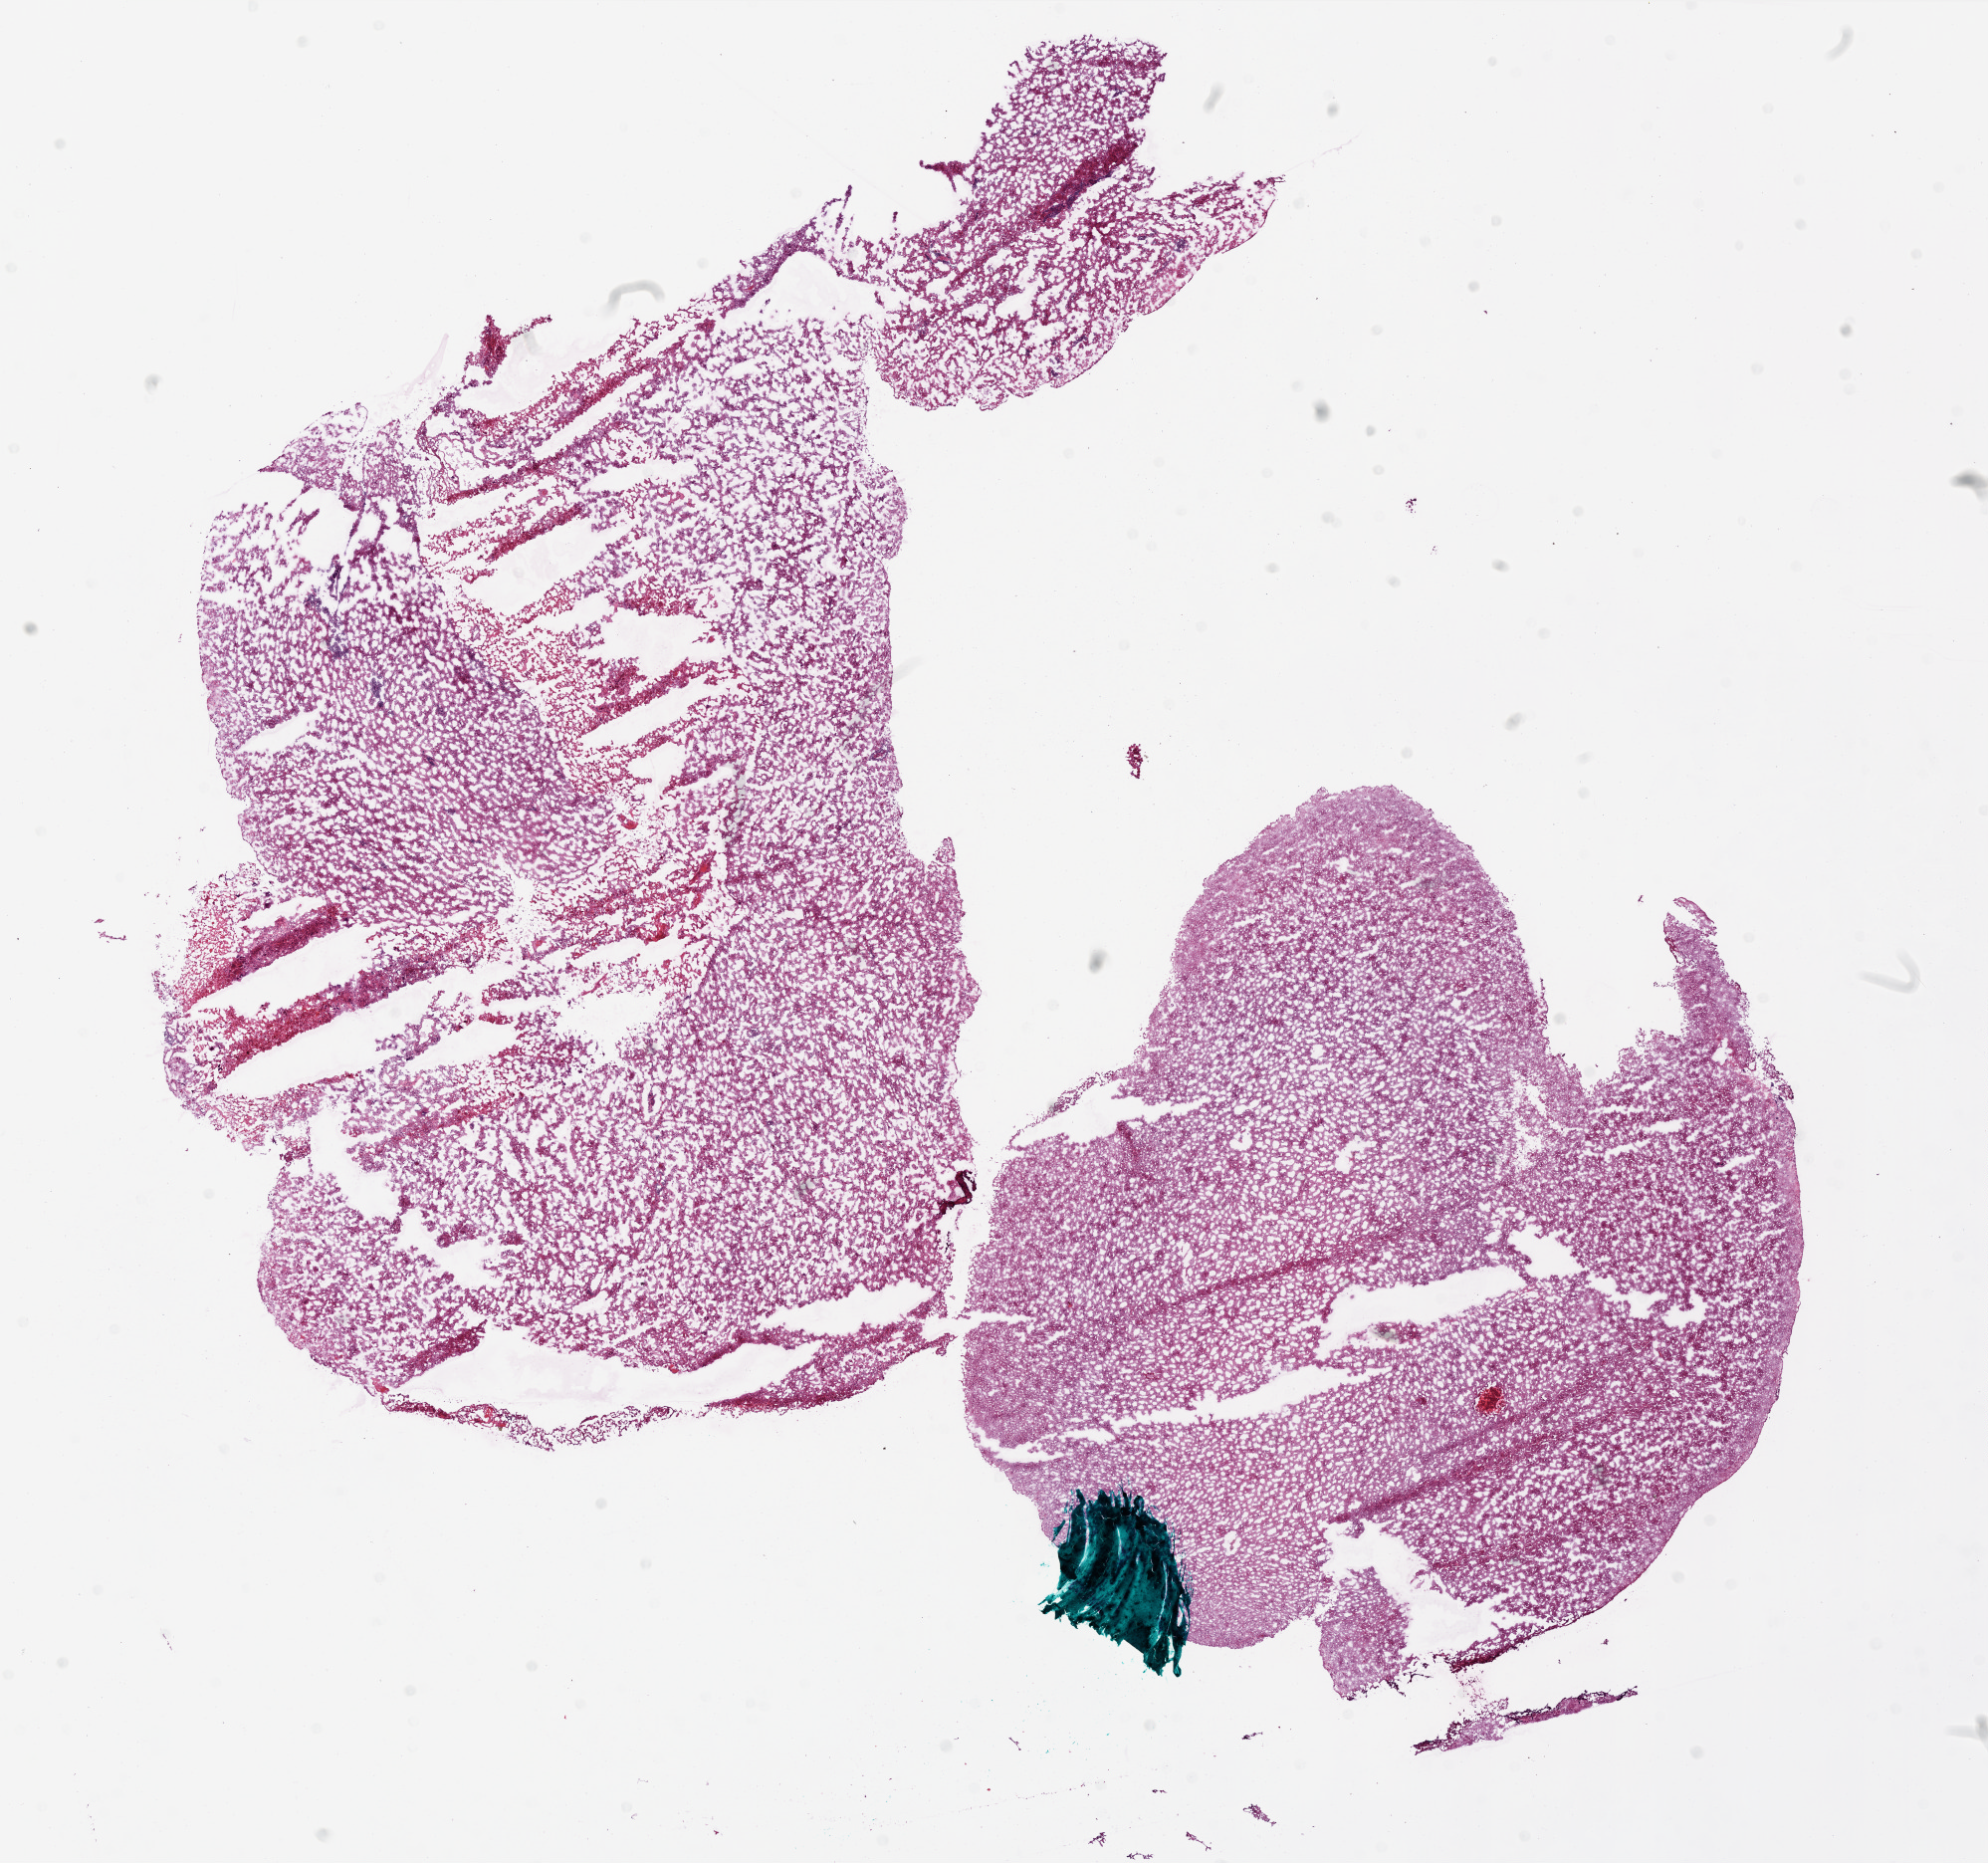
Digitized H&E-stained tissue section (whole slide) — a low-resolution overview of the entire scanned area, about 16.0 x 15.0 mm (slide scanned at 20x). Frozen section from the bottom of the tissue portion. Primary tumour sample from the brain. Patient: female, age at initial diagnosis 51 years. Slide review estimates, as recorded: tumour cells 95%, tumour nuclei 97%, normal cells 0%, stromal cells 0%, necrosis 5%. Infiltration values recorded for this section: lymphocyte infiltration 100%, monocyte infiltration 0%, neutrophil infiltration 0%.
• pathologic diagnosis: Glioblastoma